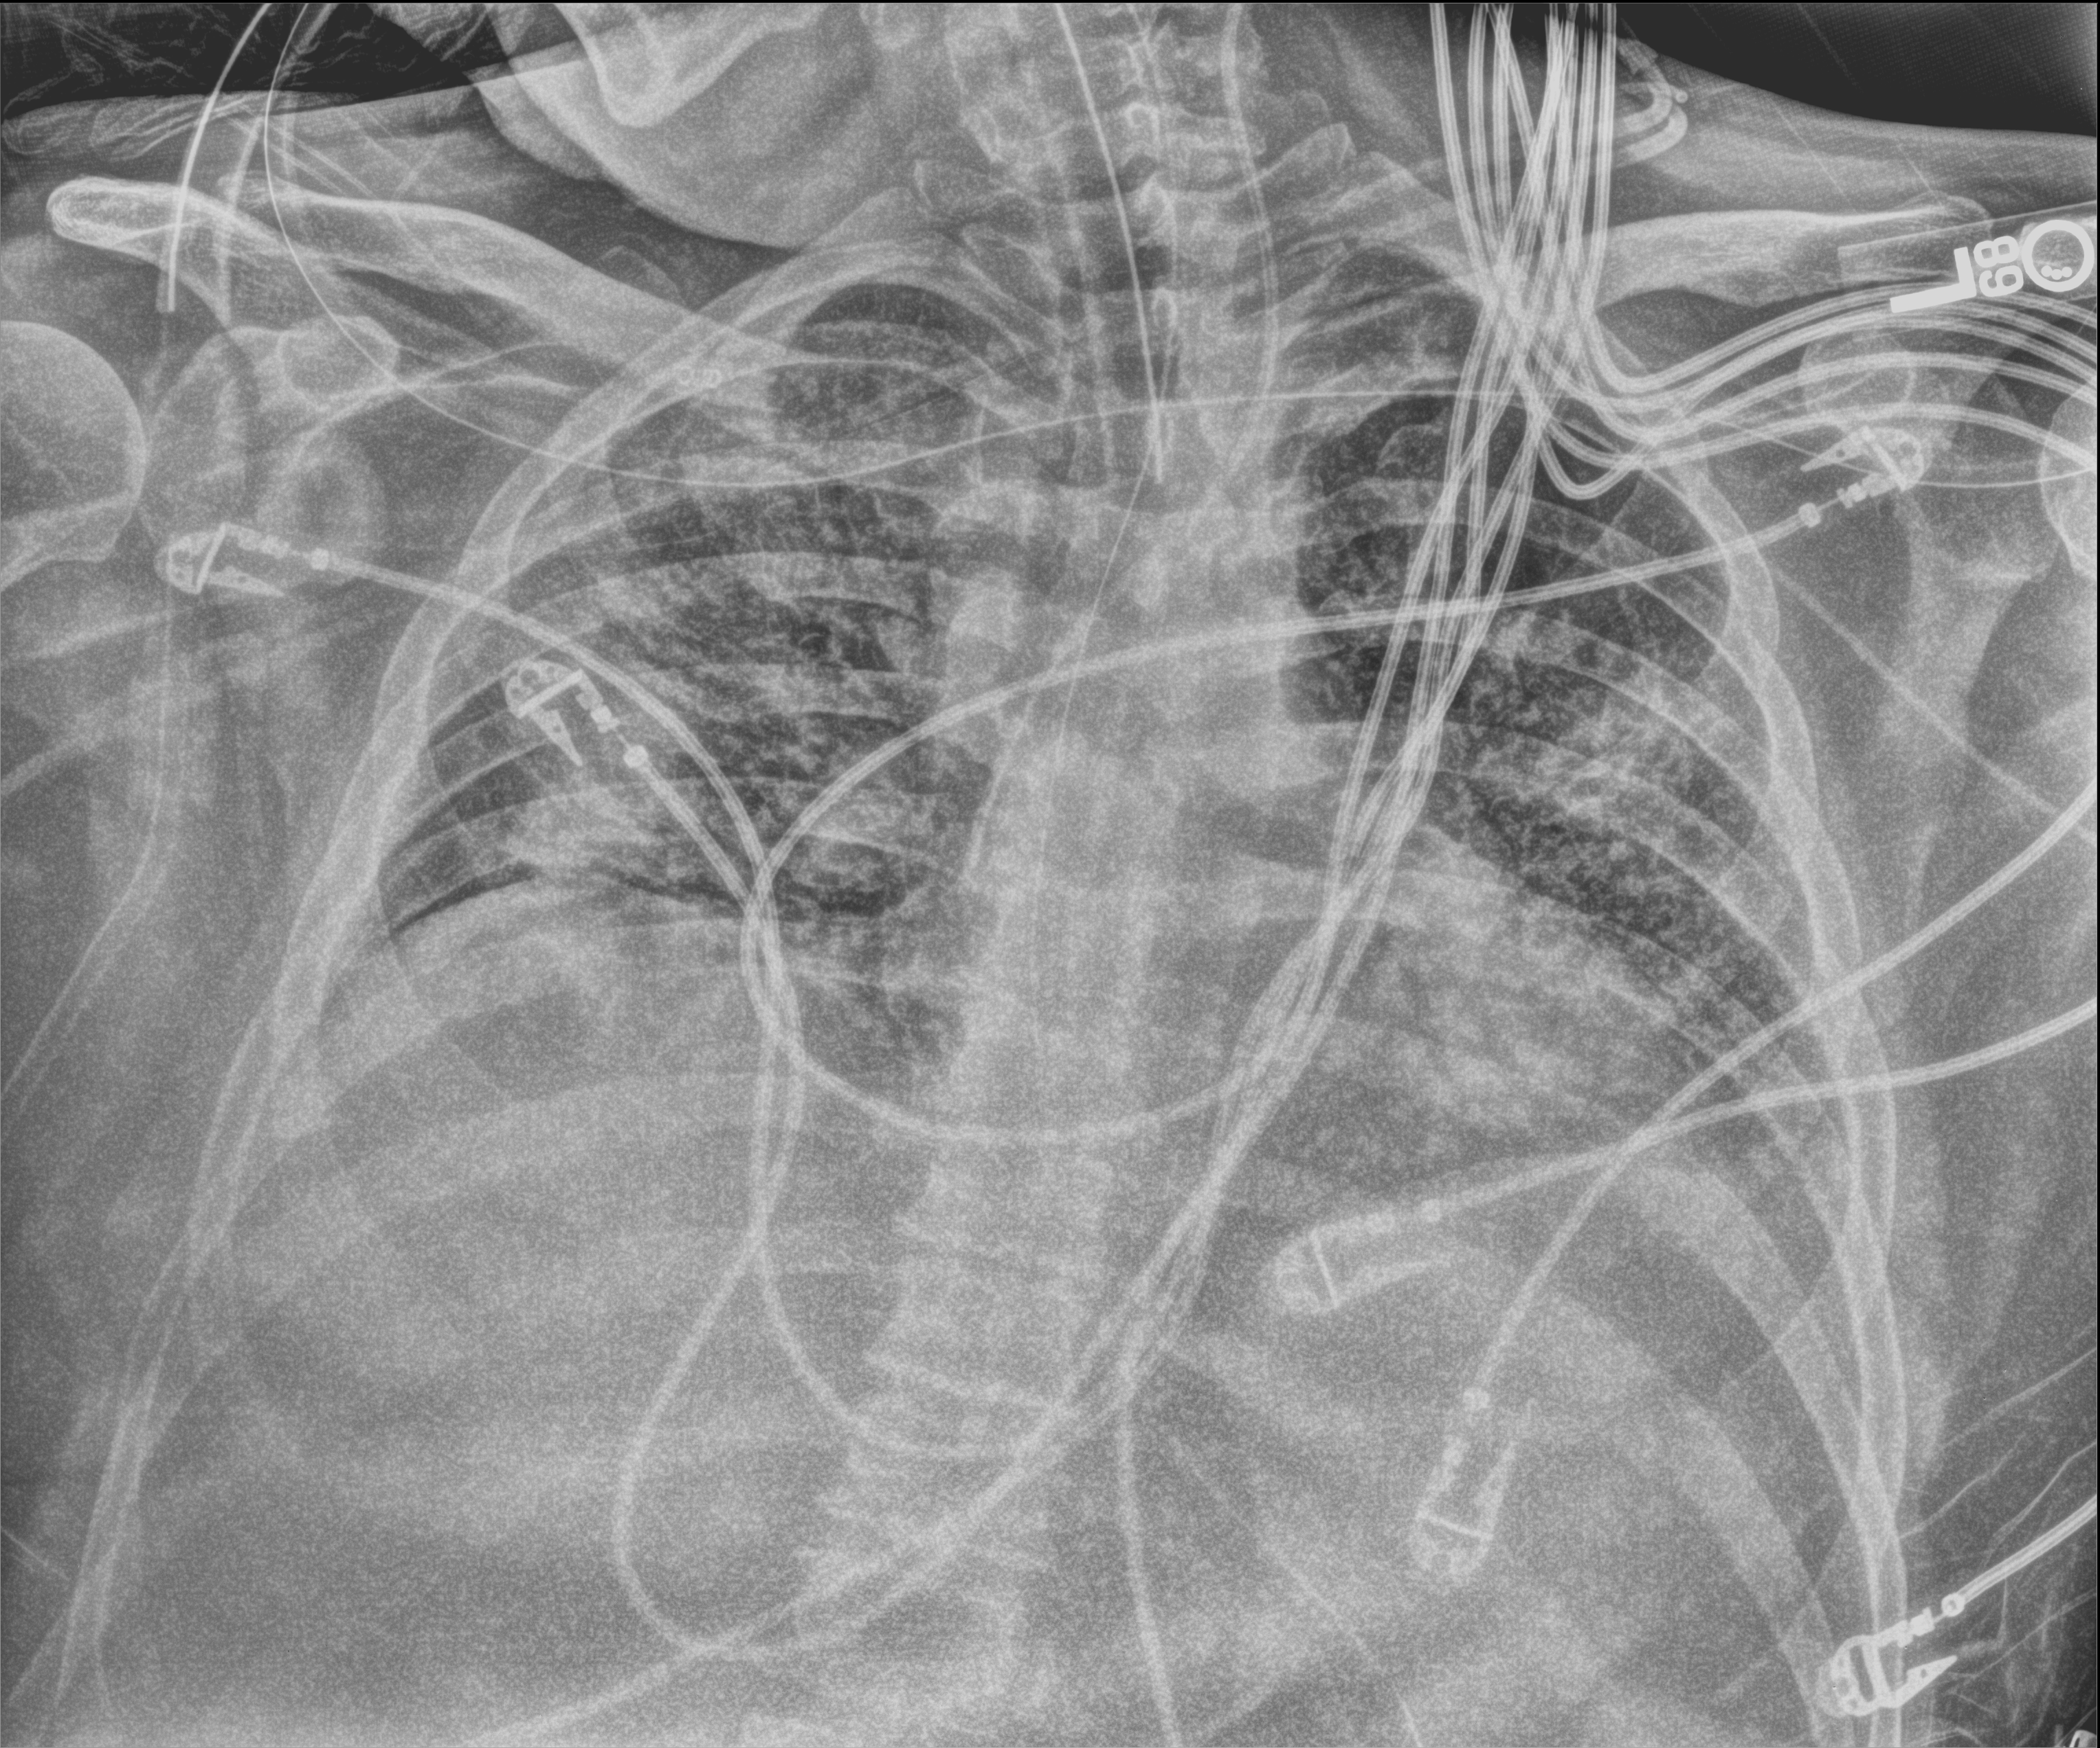
Portable chest radiograph, anteroposterior (AP) projection. Patient hospitalised with COVID-19; male, aged 18–59 years.
From the hospital-stay record, not from the radiograph (when in the stay this image was taken is not recorded): mechanically ventilated during this hospital stay: yes.